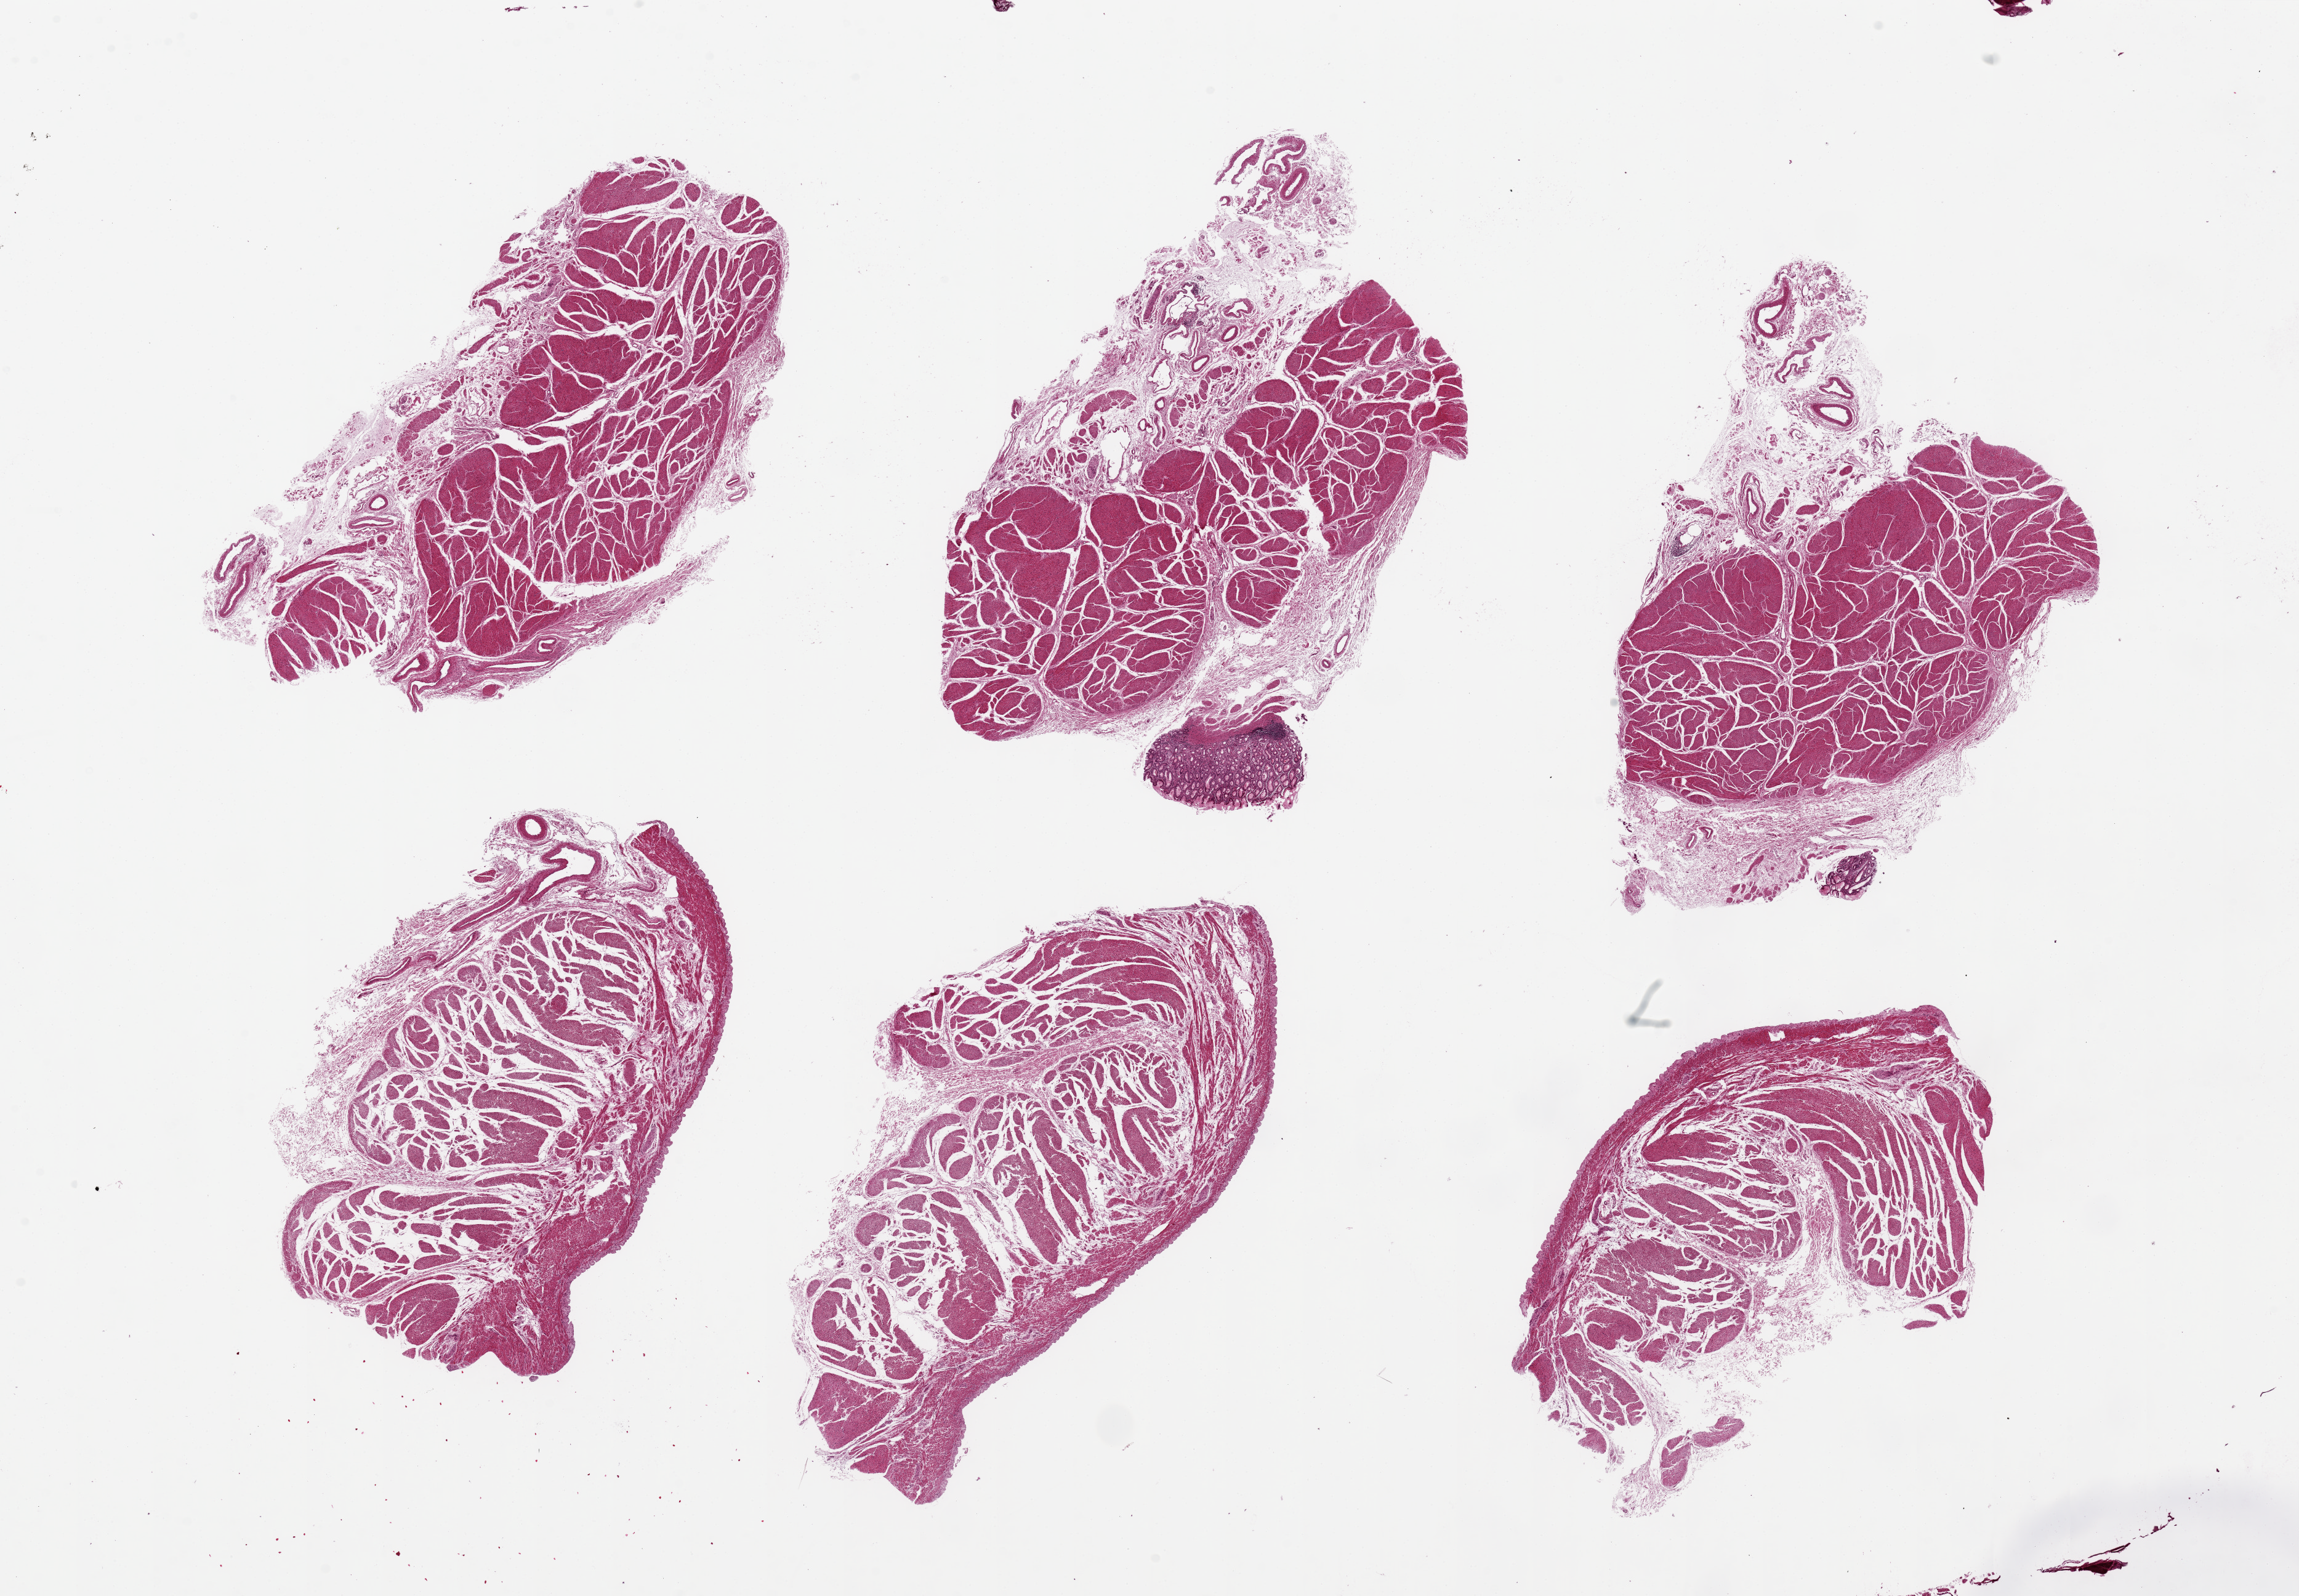
Whole-slide image, H&E stain — a low-resolution overview of the entire scanned area, about 29.5 x 20.5 mm (acquisition: 20x scan), PAXgene-fixed, paraffin-embedded tissue, target tissue: stomach, tissue donor sample. Female donor.
Review note (as recorded): 6 pieces, up to 9x5mm; 5 of 6 are all muscle; only minute pieces of mucosa present.